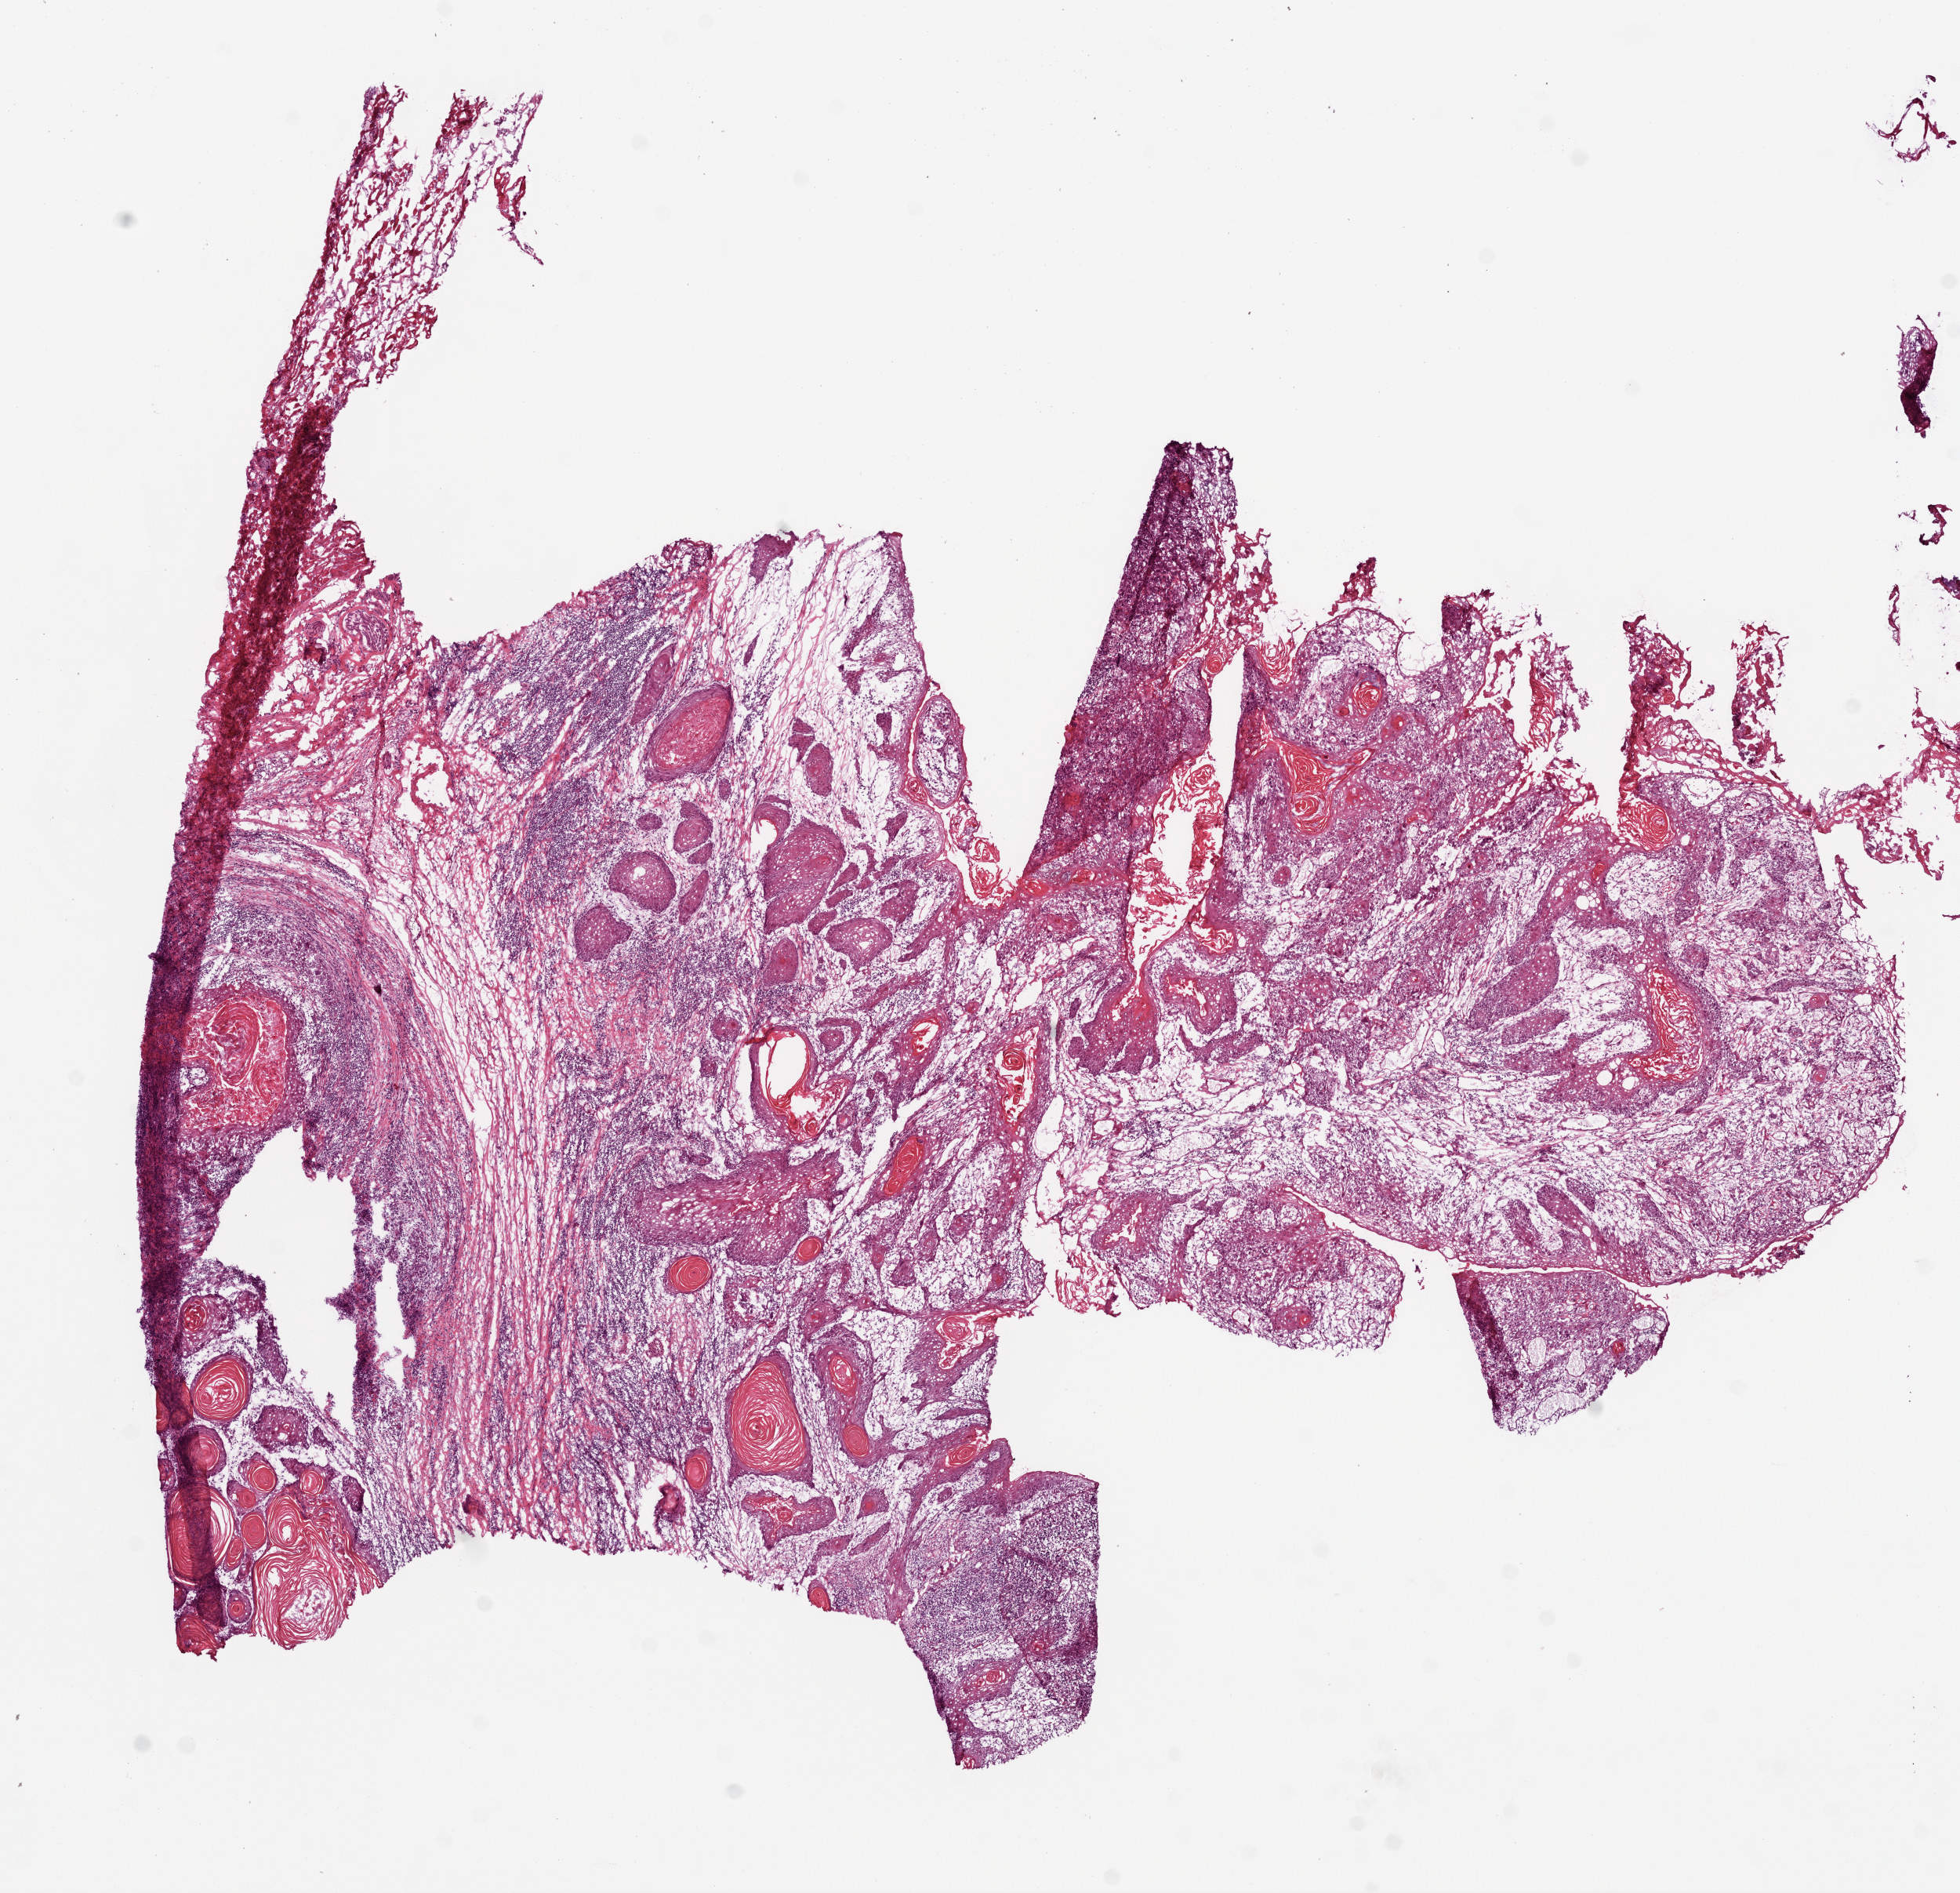
Digitized Hematoxylin and eosin (H&E) stained tissue section (whole slide) — whole scanned area (about 10.0 x 9.7 mm) shown as a low-resolution overview, frozen section from the bottom of the tissue portion, head and neck, primary tumour sample. Male patient; age at initial diagnosis 60 years. Histologic grade: G2 (moderately differentiated). Composition of this section per pathologist review: tumour cells 60%, tumour nuclei 70%, normal cells 0%, stromal cells 40%, necrosis 0%.
• TNM: T2 N0
• AJCC pathologic stage: II (7th edition)
• diagnosis: Squamous cell carcinoma, NOS